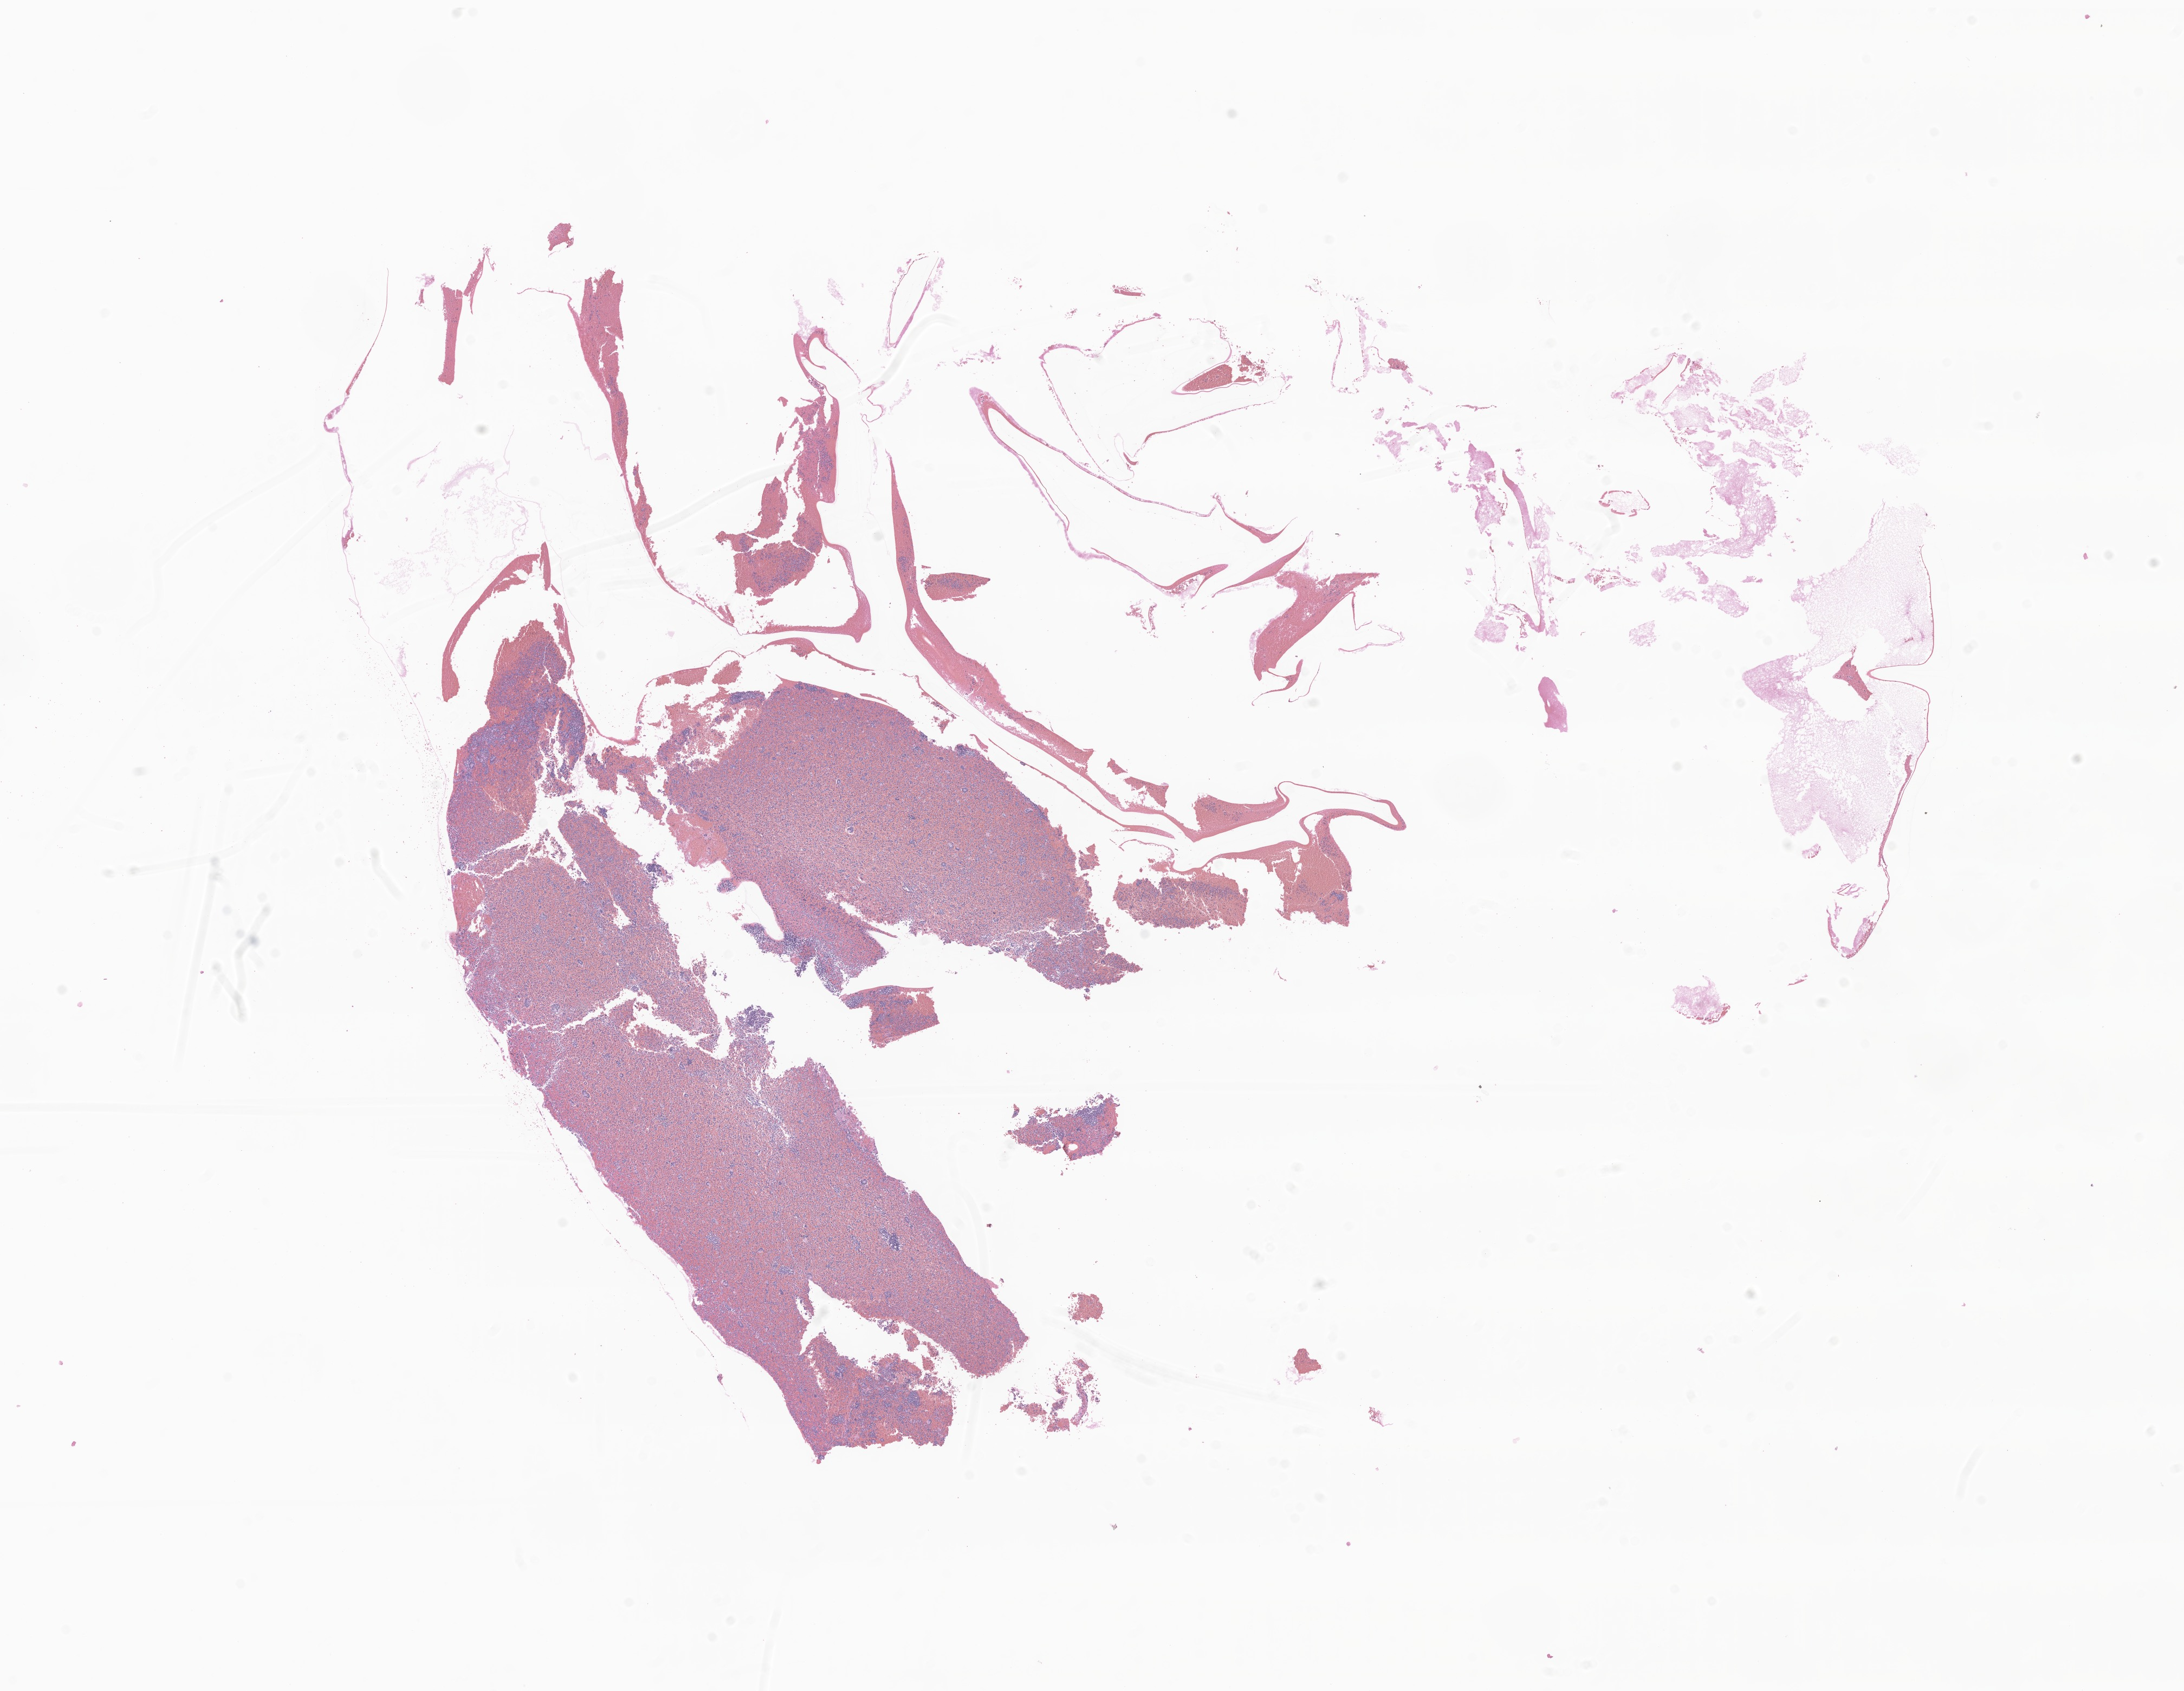
Digitized H&E-stained section of tumor tissue from the soft tissue, a low-resolution overview of the entire scanned area, about 17.0 x 13.2 mm; formalin-fixed, paraffin-embedded (FFPE) tissue. Patient: male, age 48 months (4 years).
Recorded diagnosis: Alveolar rhabdomyosarcoma.